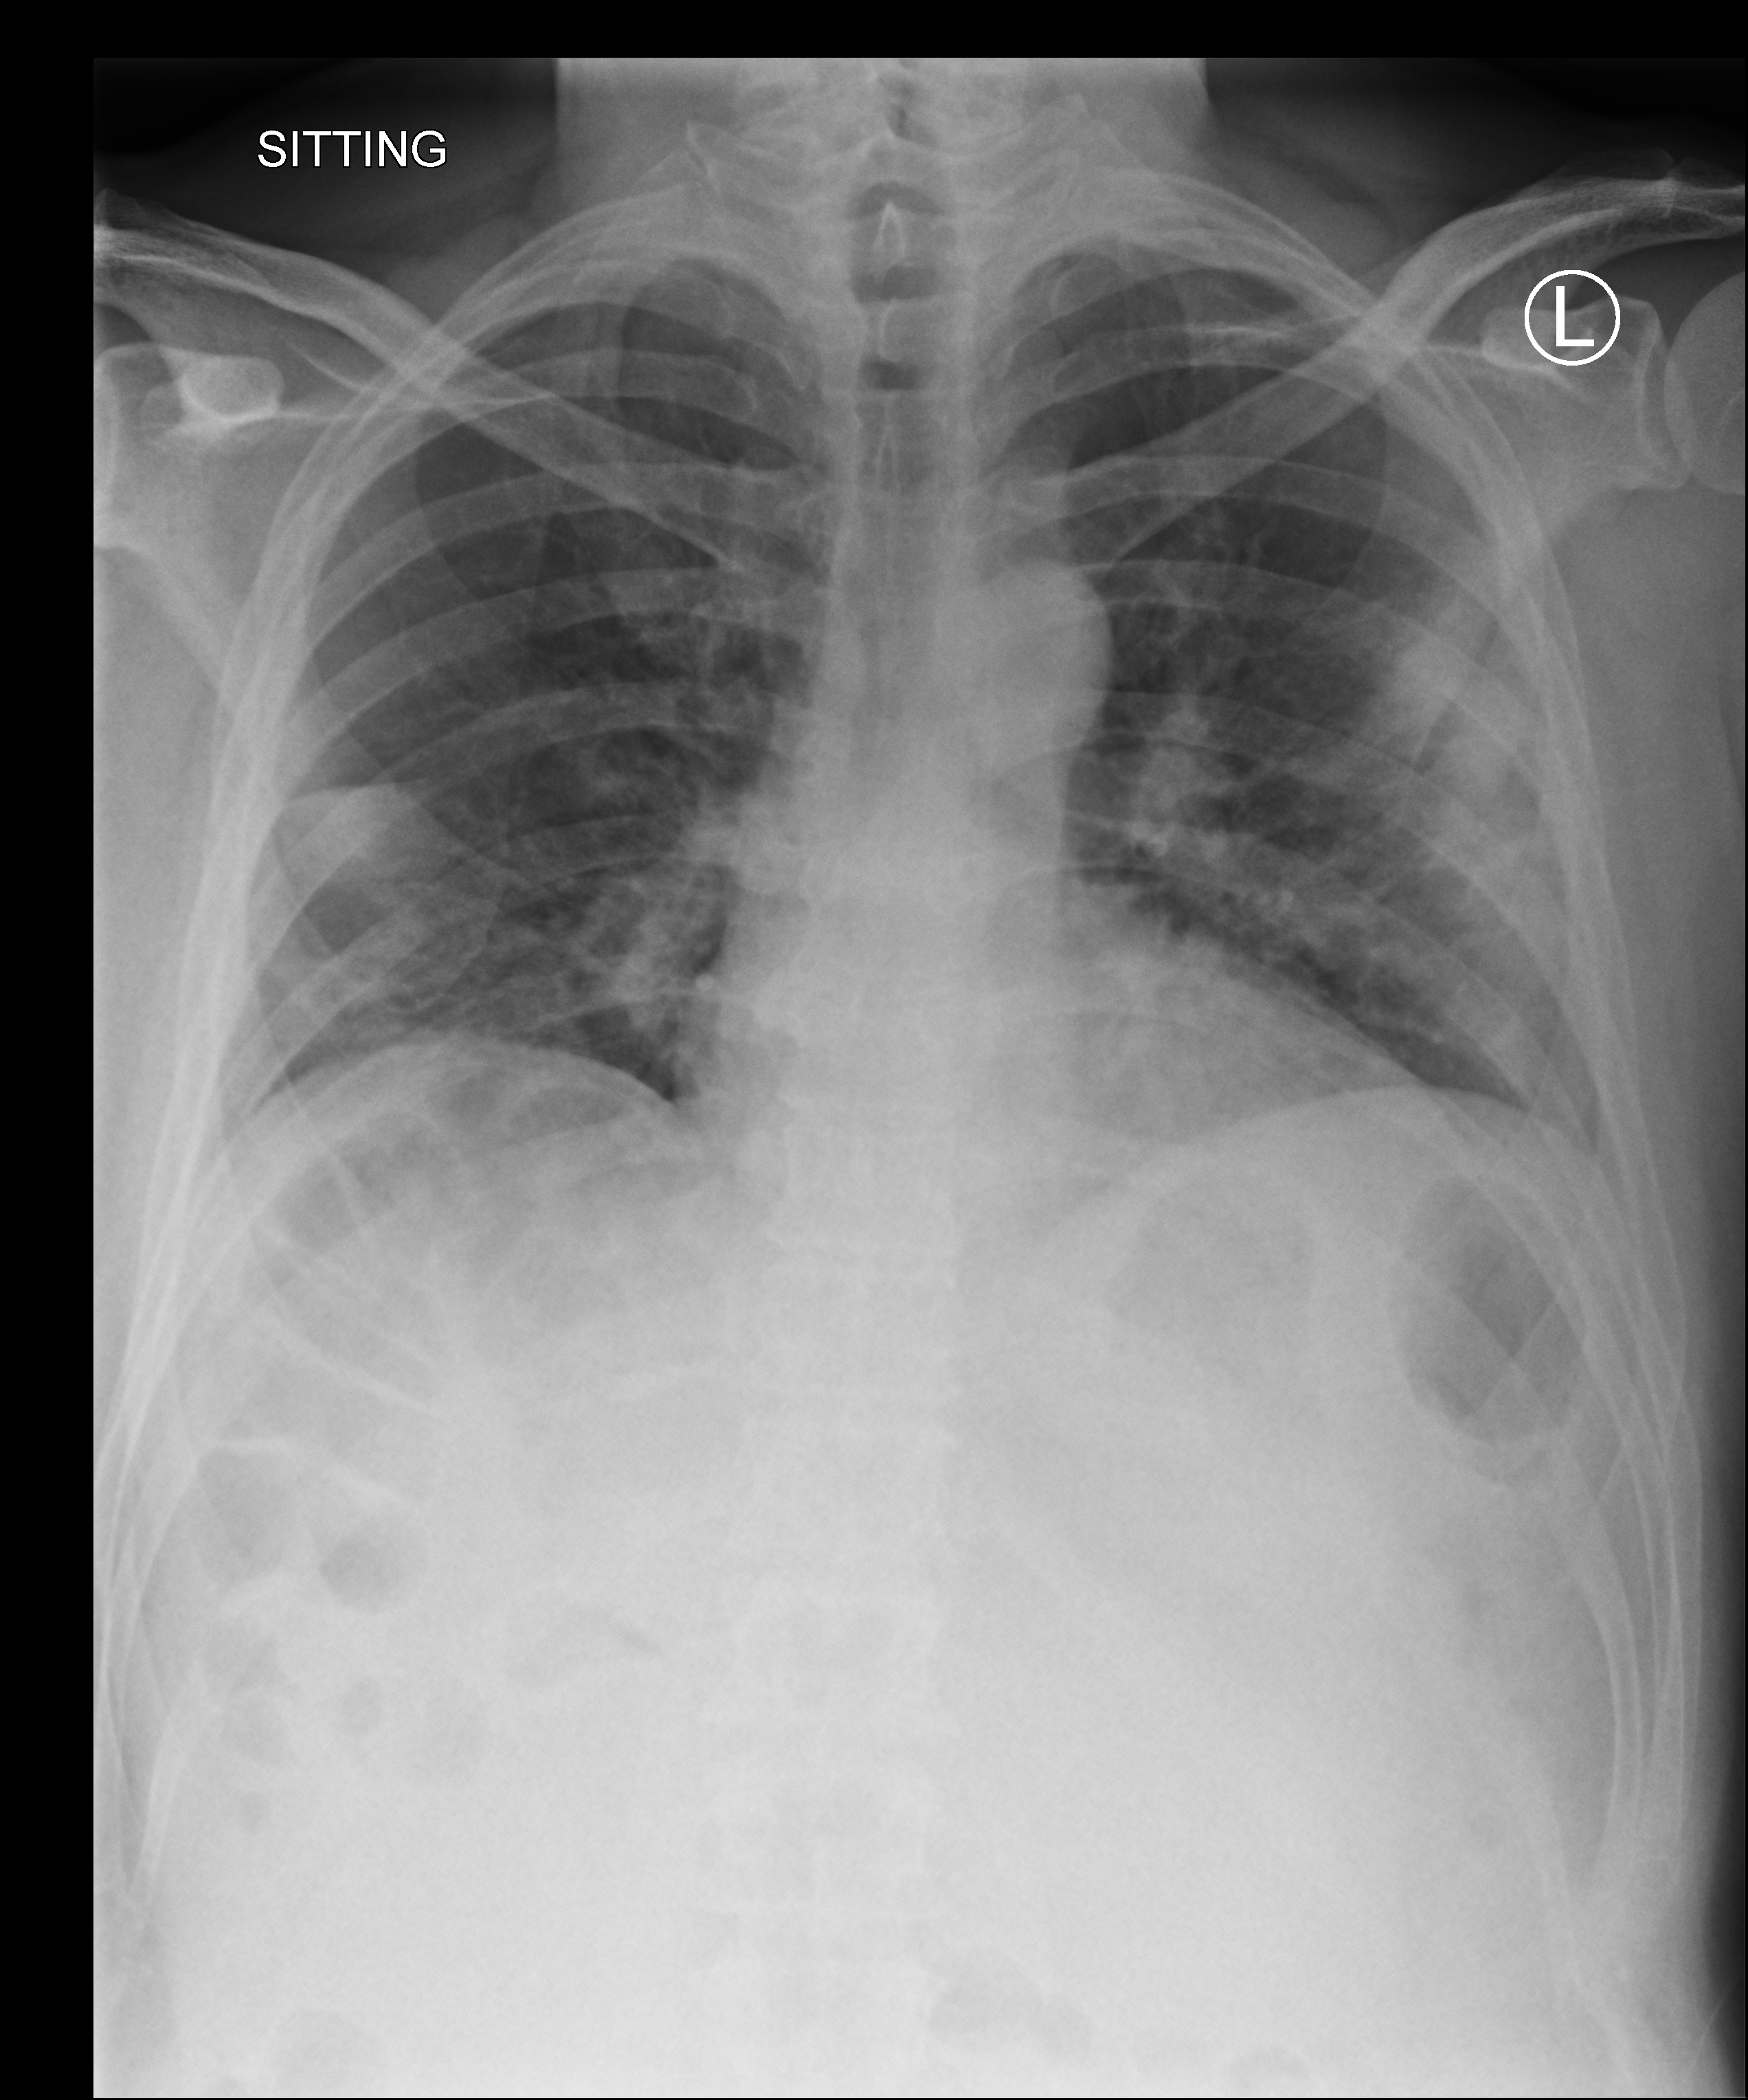
Portable chest radiograph, anteroposterior (AP) projection. Patient hospitalised with COVID-19; male, aged 18–59 years.
From the hospital-stay record, not from the radiograph (when in the stay this image was taken is not recorded): length of hospital stay: 1 day.